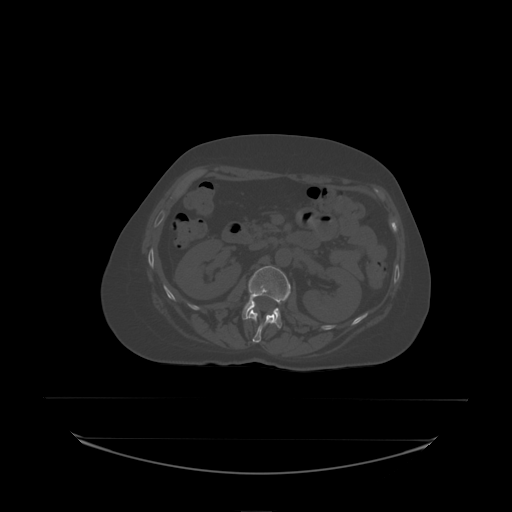
CT including the spine, one axial slice. Slice 77 of 242 in the series (ordered by position). Bone window (W 1800 / L 400 HU). 2.5 mm slice thickness. 512 × 512 image matrix, field of view 500 × 500 mm. Female patient, age 53 years. Case-level facts recorded for this patient, not image findings: primary cancer: lung.
Annotated regions visible in this slice (semi-automatic segmentation, software-assisted and operator-edited):
- L1 vertebra: bounding box (x1, y1, x2, y2) in pixels: (249, 309, 275, 338)
- L2 vertebra: (243, 266, 291, 329)